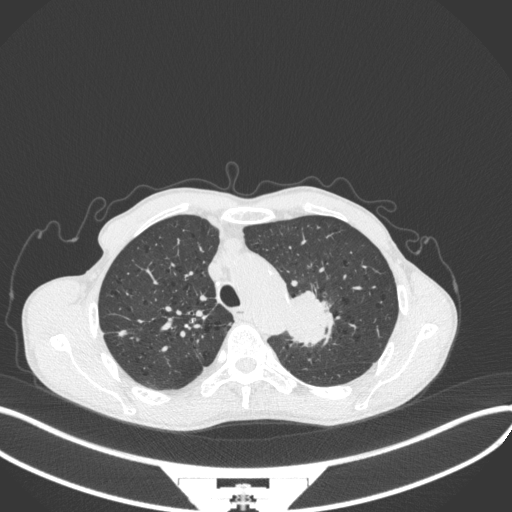
Chest CT, one axial slice; position 320 of 394 along the scan axis; reconstruction kernel B31f; lung window (W 1500 / L -600 HU); 512 × 512 image matrix, field of view 400 × 400 mm. Male patient, age 65 years. Case-level facts recorded for this patient, not image findings: clinical TNM (as recorded): T2b N0 M0.
Outlined on this slice (rectangle marked by the reading radiologist):
- lung tumour (recorded histology: adenocarcinoma): bounding box <283,286,337,350> (left, top, right, bottom; pixels)